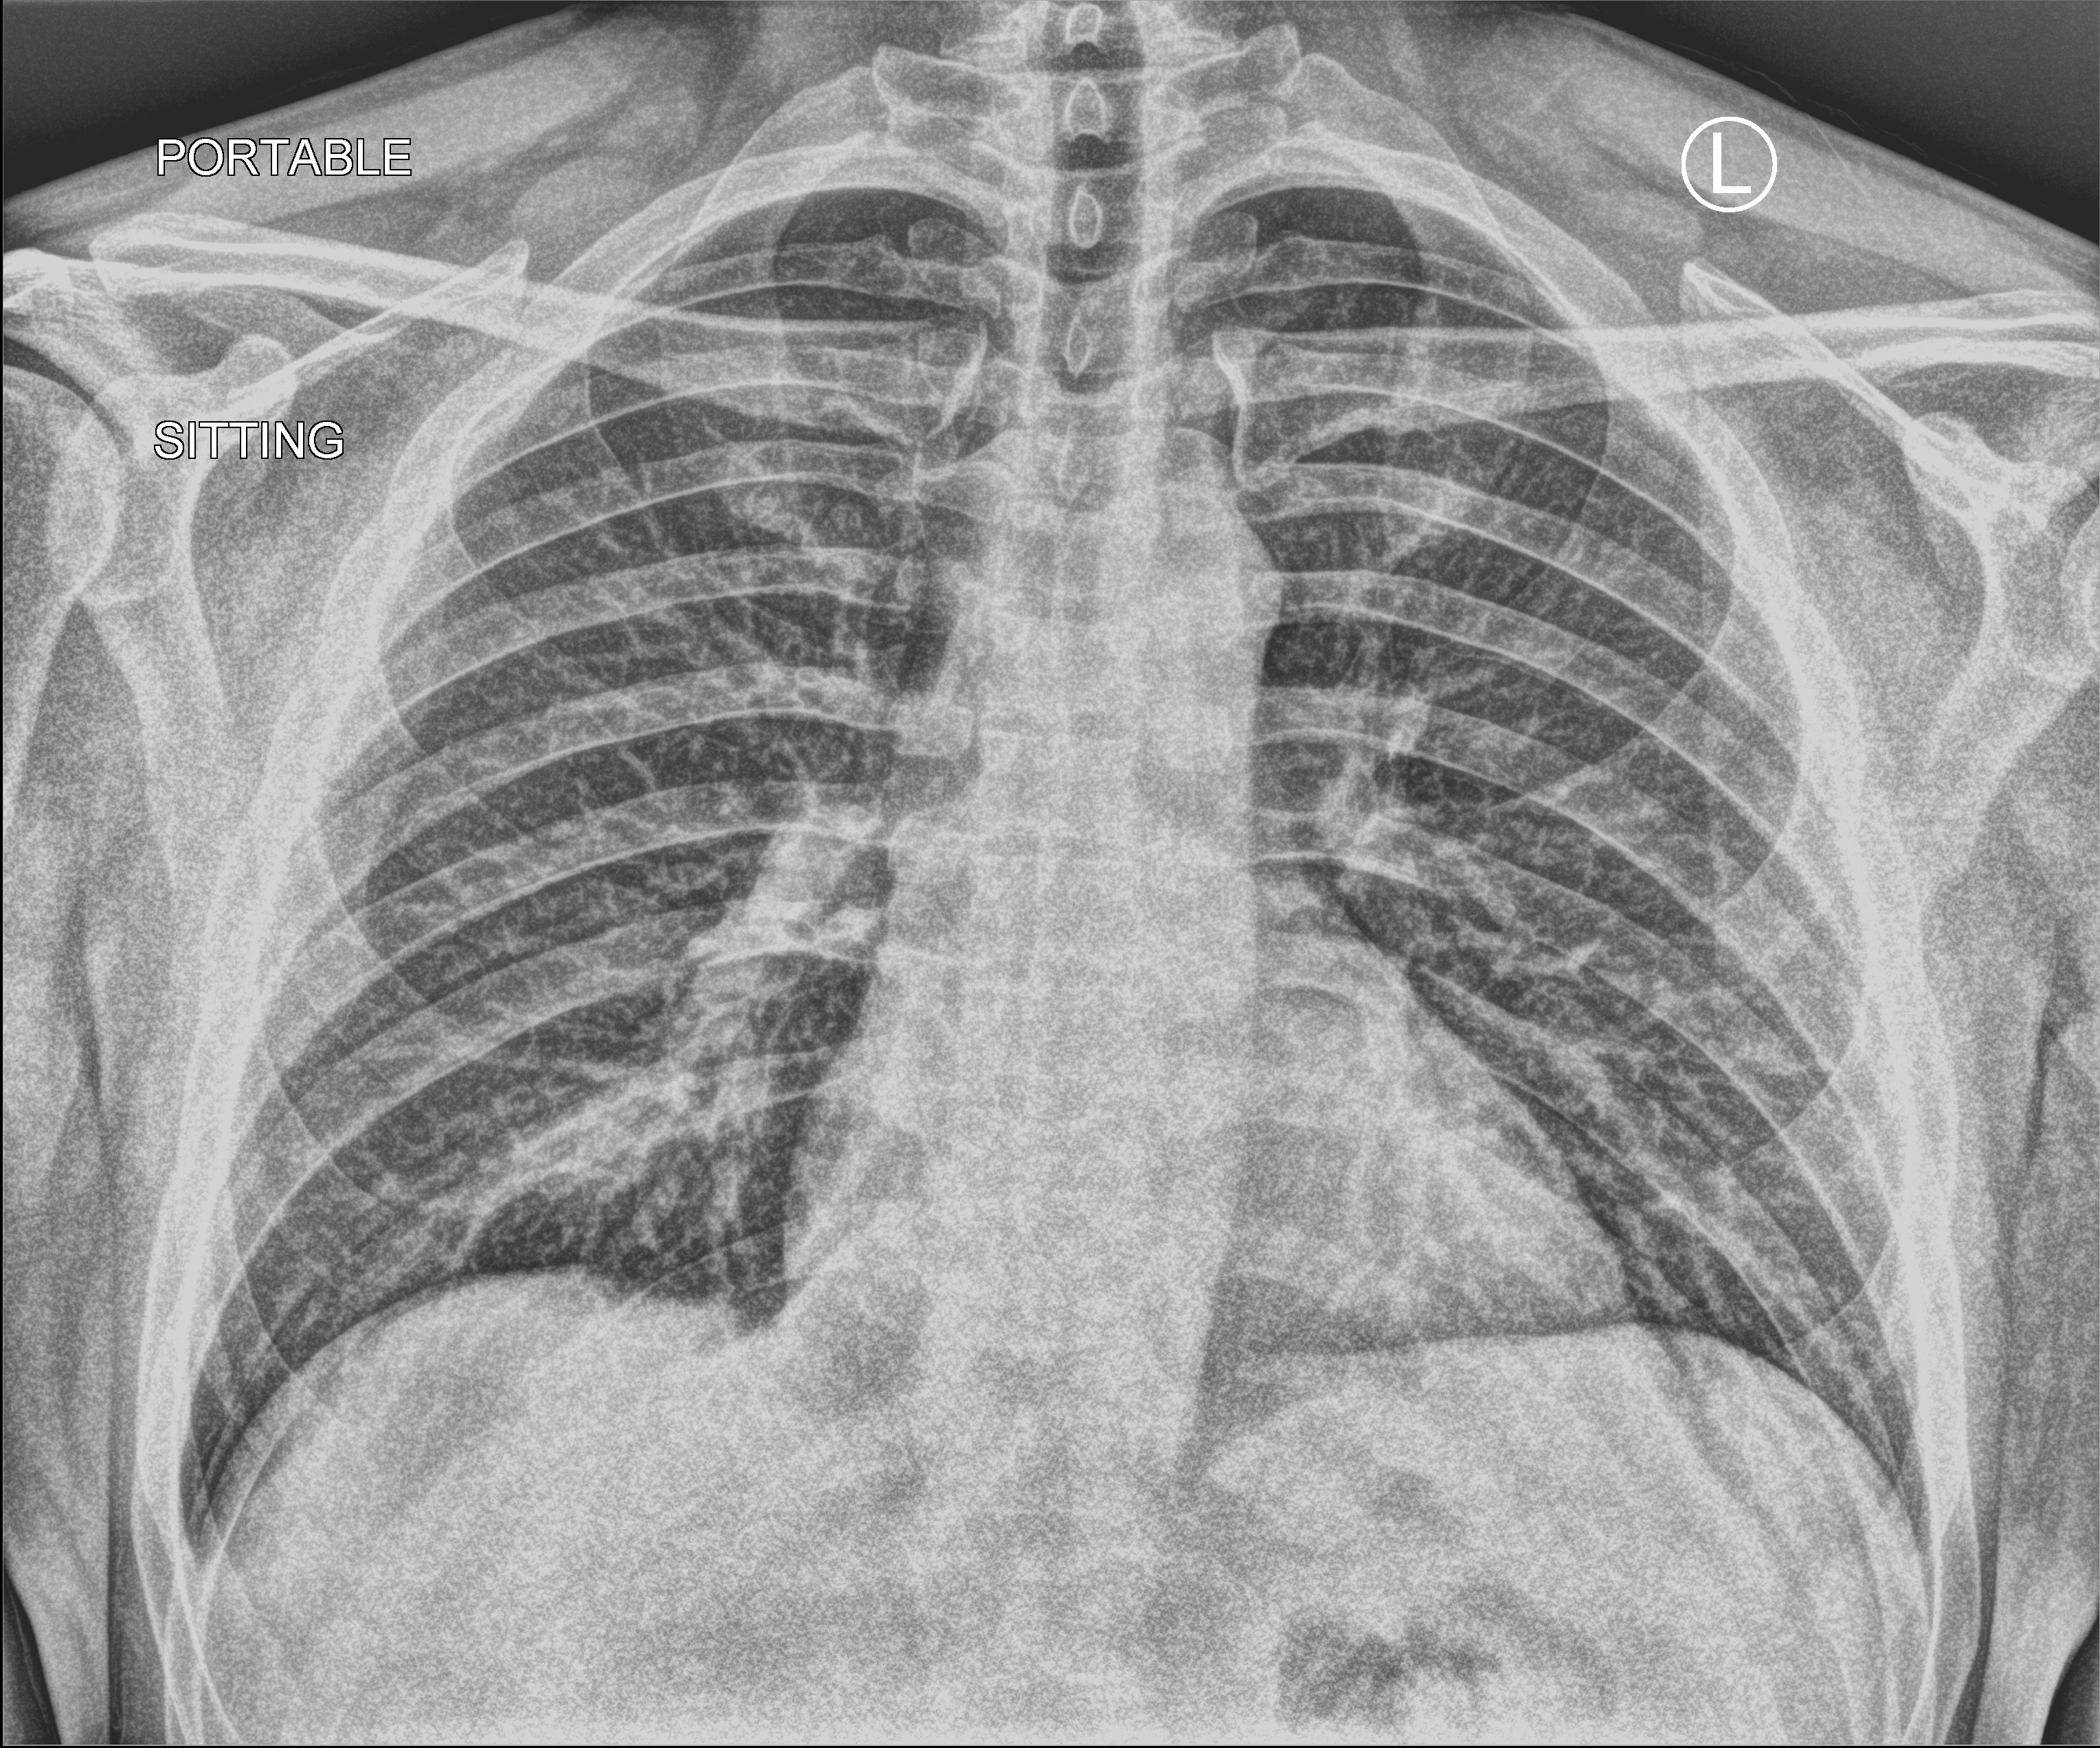
Portable chest radiograph. Patient hospitalised with COVID-19; male, aged 18–59 years.
Hospital-stay facts (about this admission, not read from this image; timing relative to this image not recorded): admitted to intensive care during this hospital stay: no; chronic kidney disease (admission record): no.